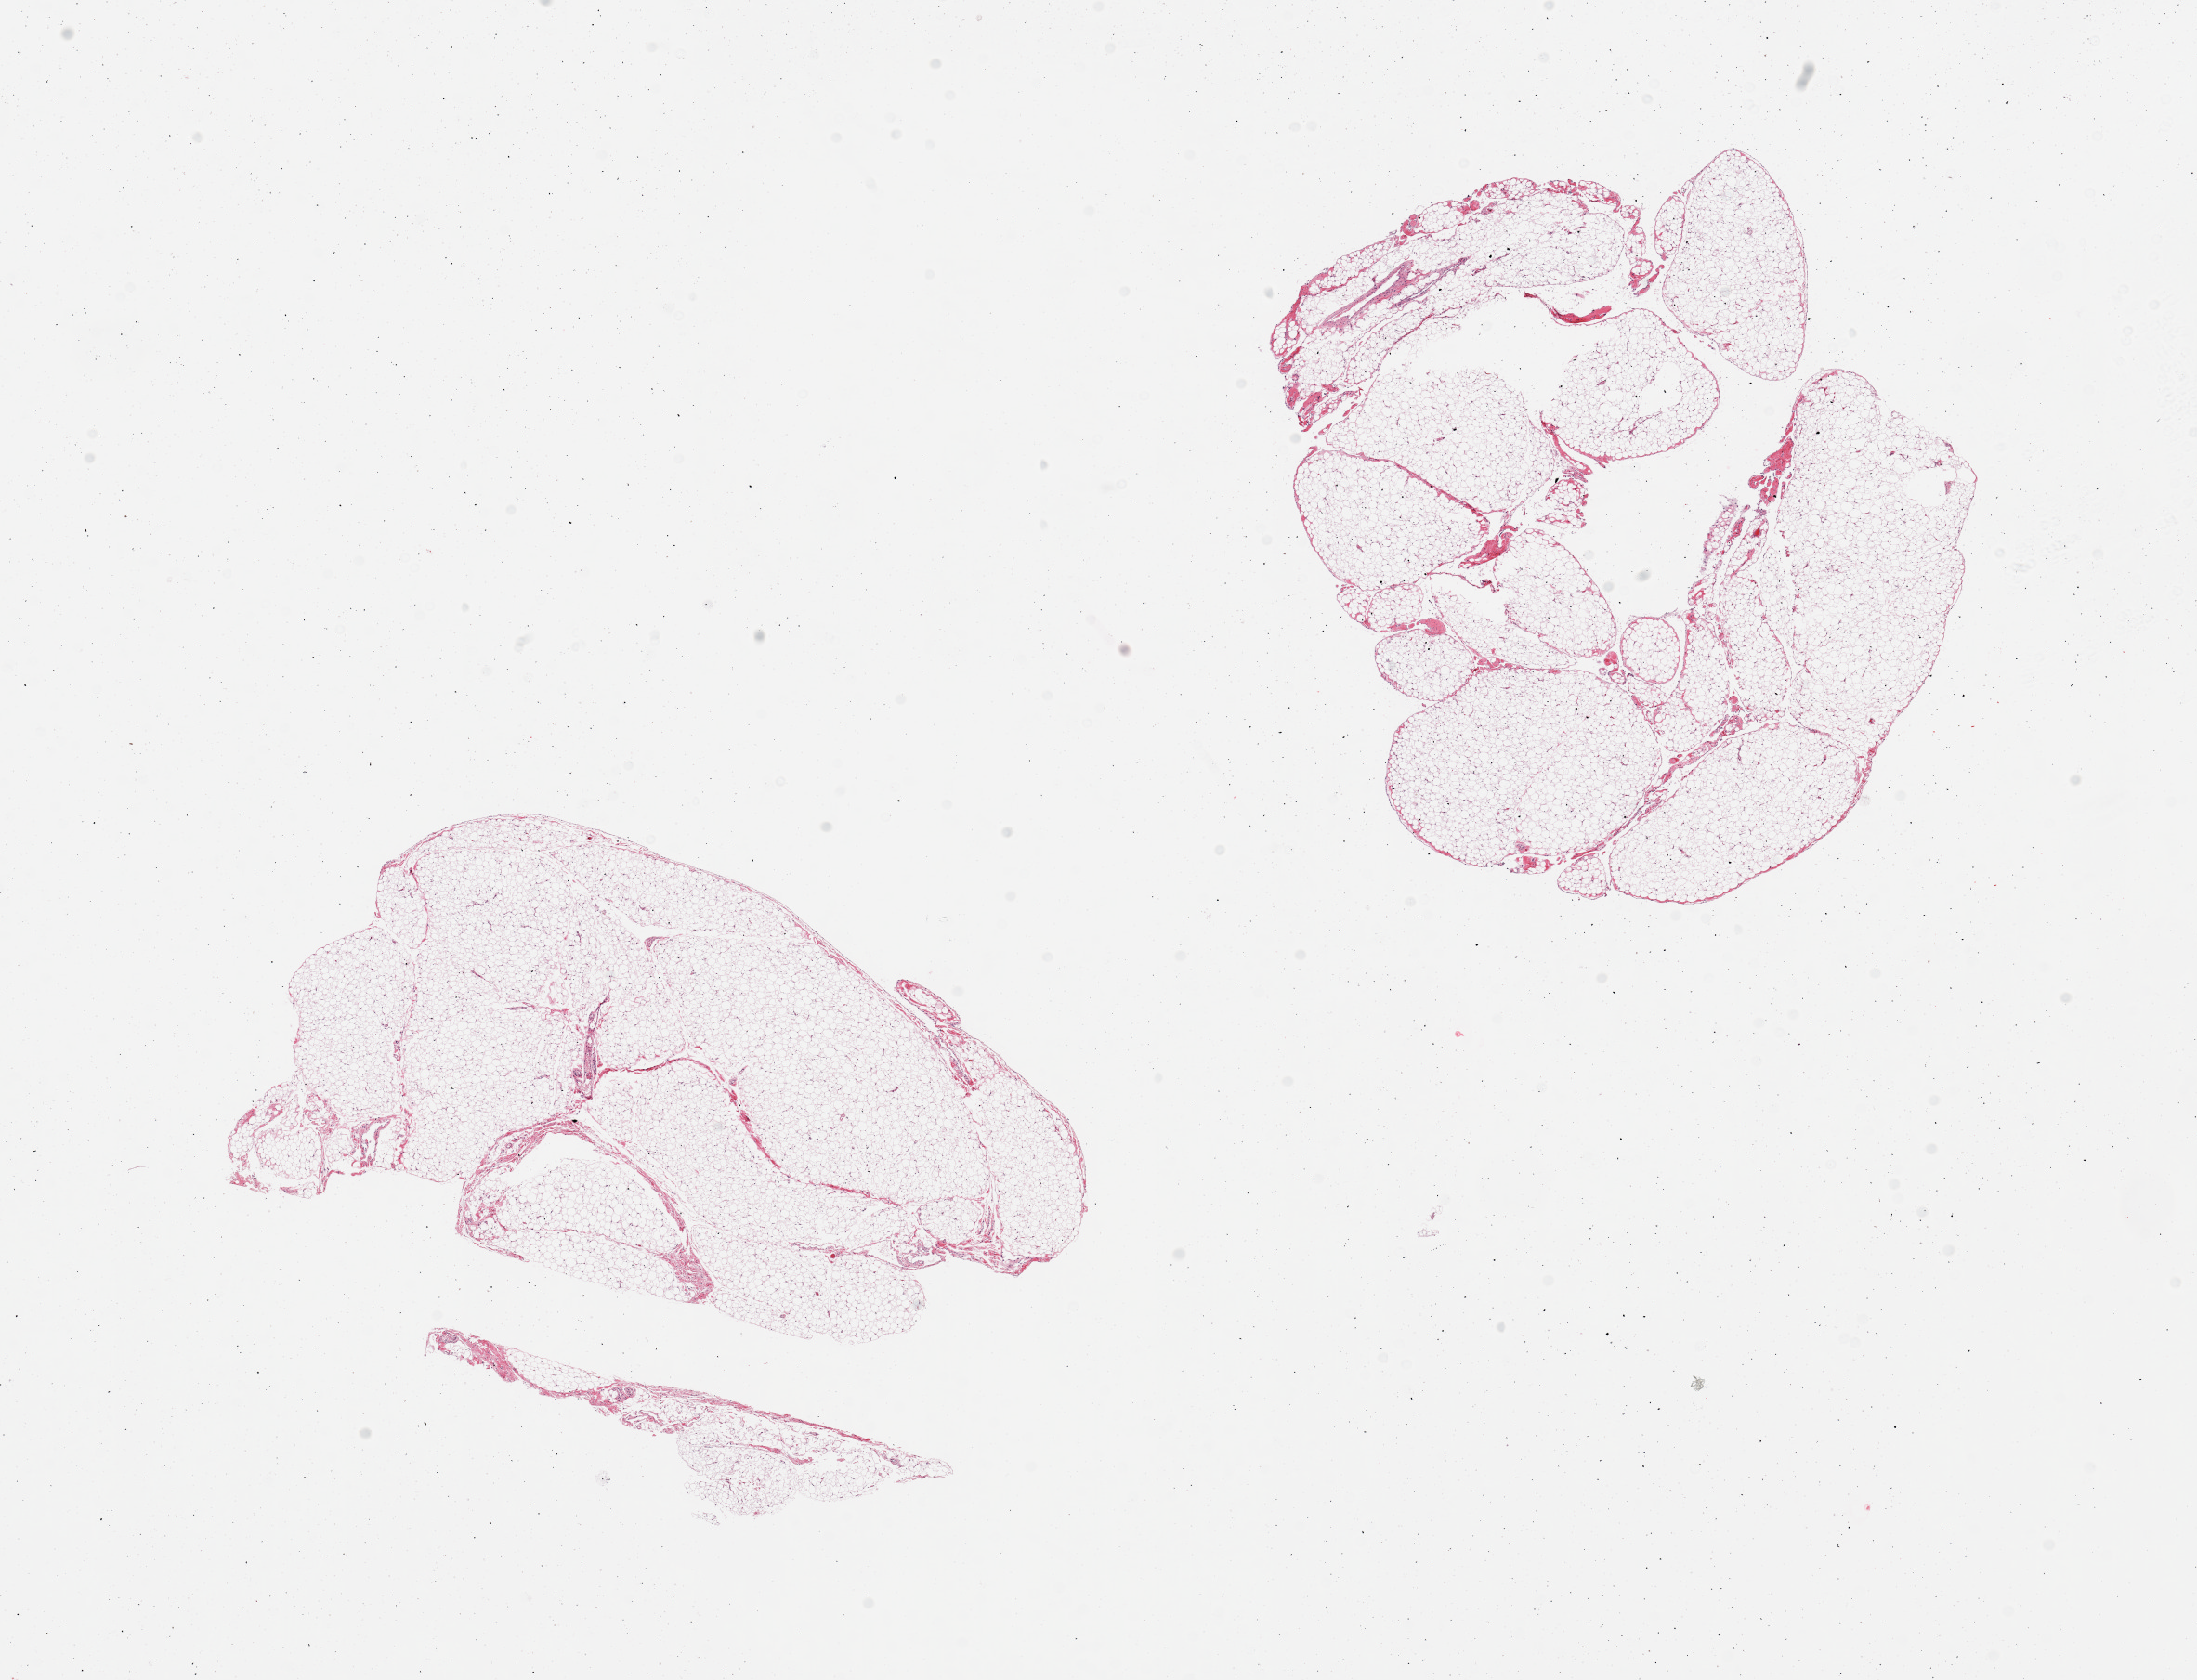
Hematoxylin and eosin (H&E) whole-slide image — a low-resolution overview of the entire scanned area, about 18.7 x 14.3 mm (acquisition: 20x scan); PAXgene-fixed paraffin-embedded (PFPE) section; sampled site (target tissue): omentum; tissue donor sample. Donor: female.
Pathologist's review note for this sample: 2 pieces.